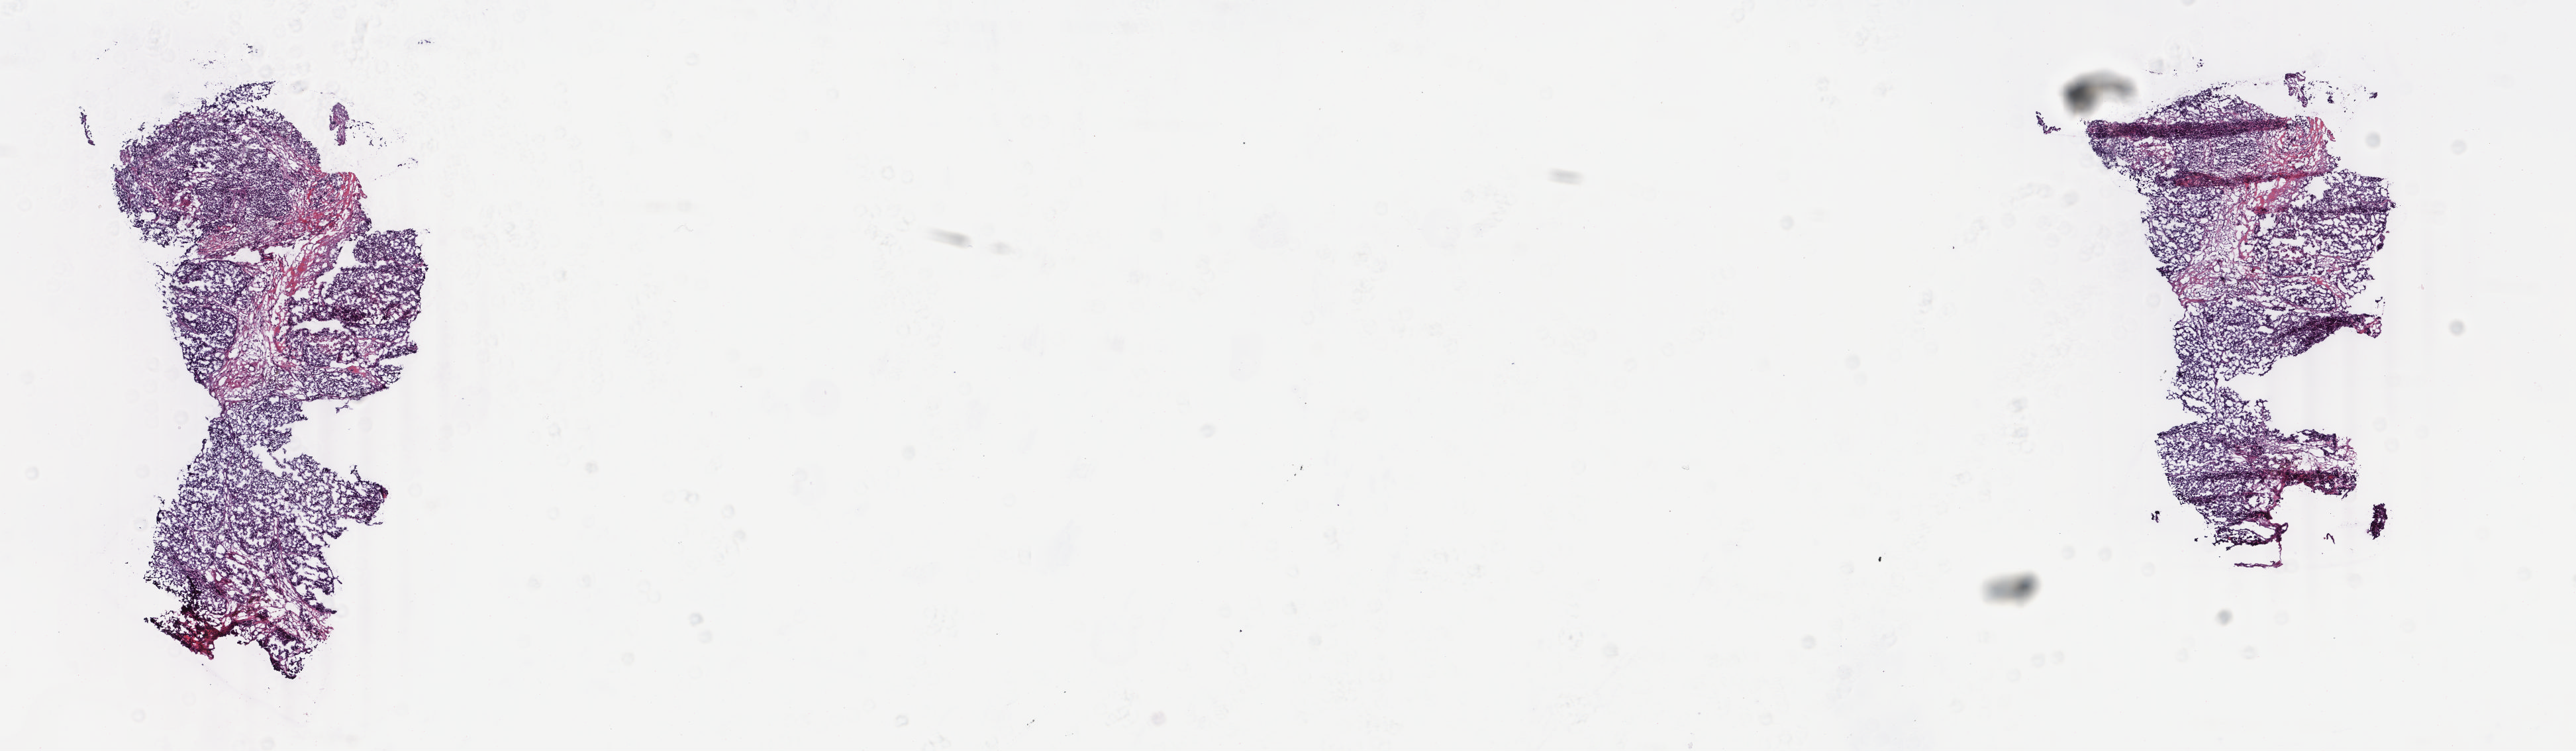
H&E-stained whole-slide image, a low-resolution overview of the entire scanned area, about 15.5 x 4.5 mm, frozen section, sample: primary tumour, breast. Female, age 58 years at initial diagnosis.
Histologic diagnosis: Infiltrating duct carcinoma, NOS.